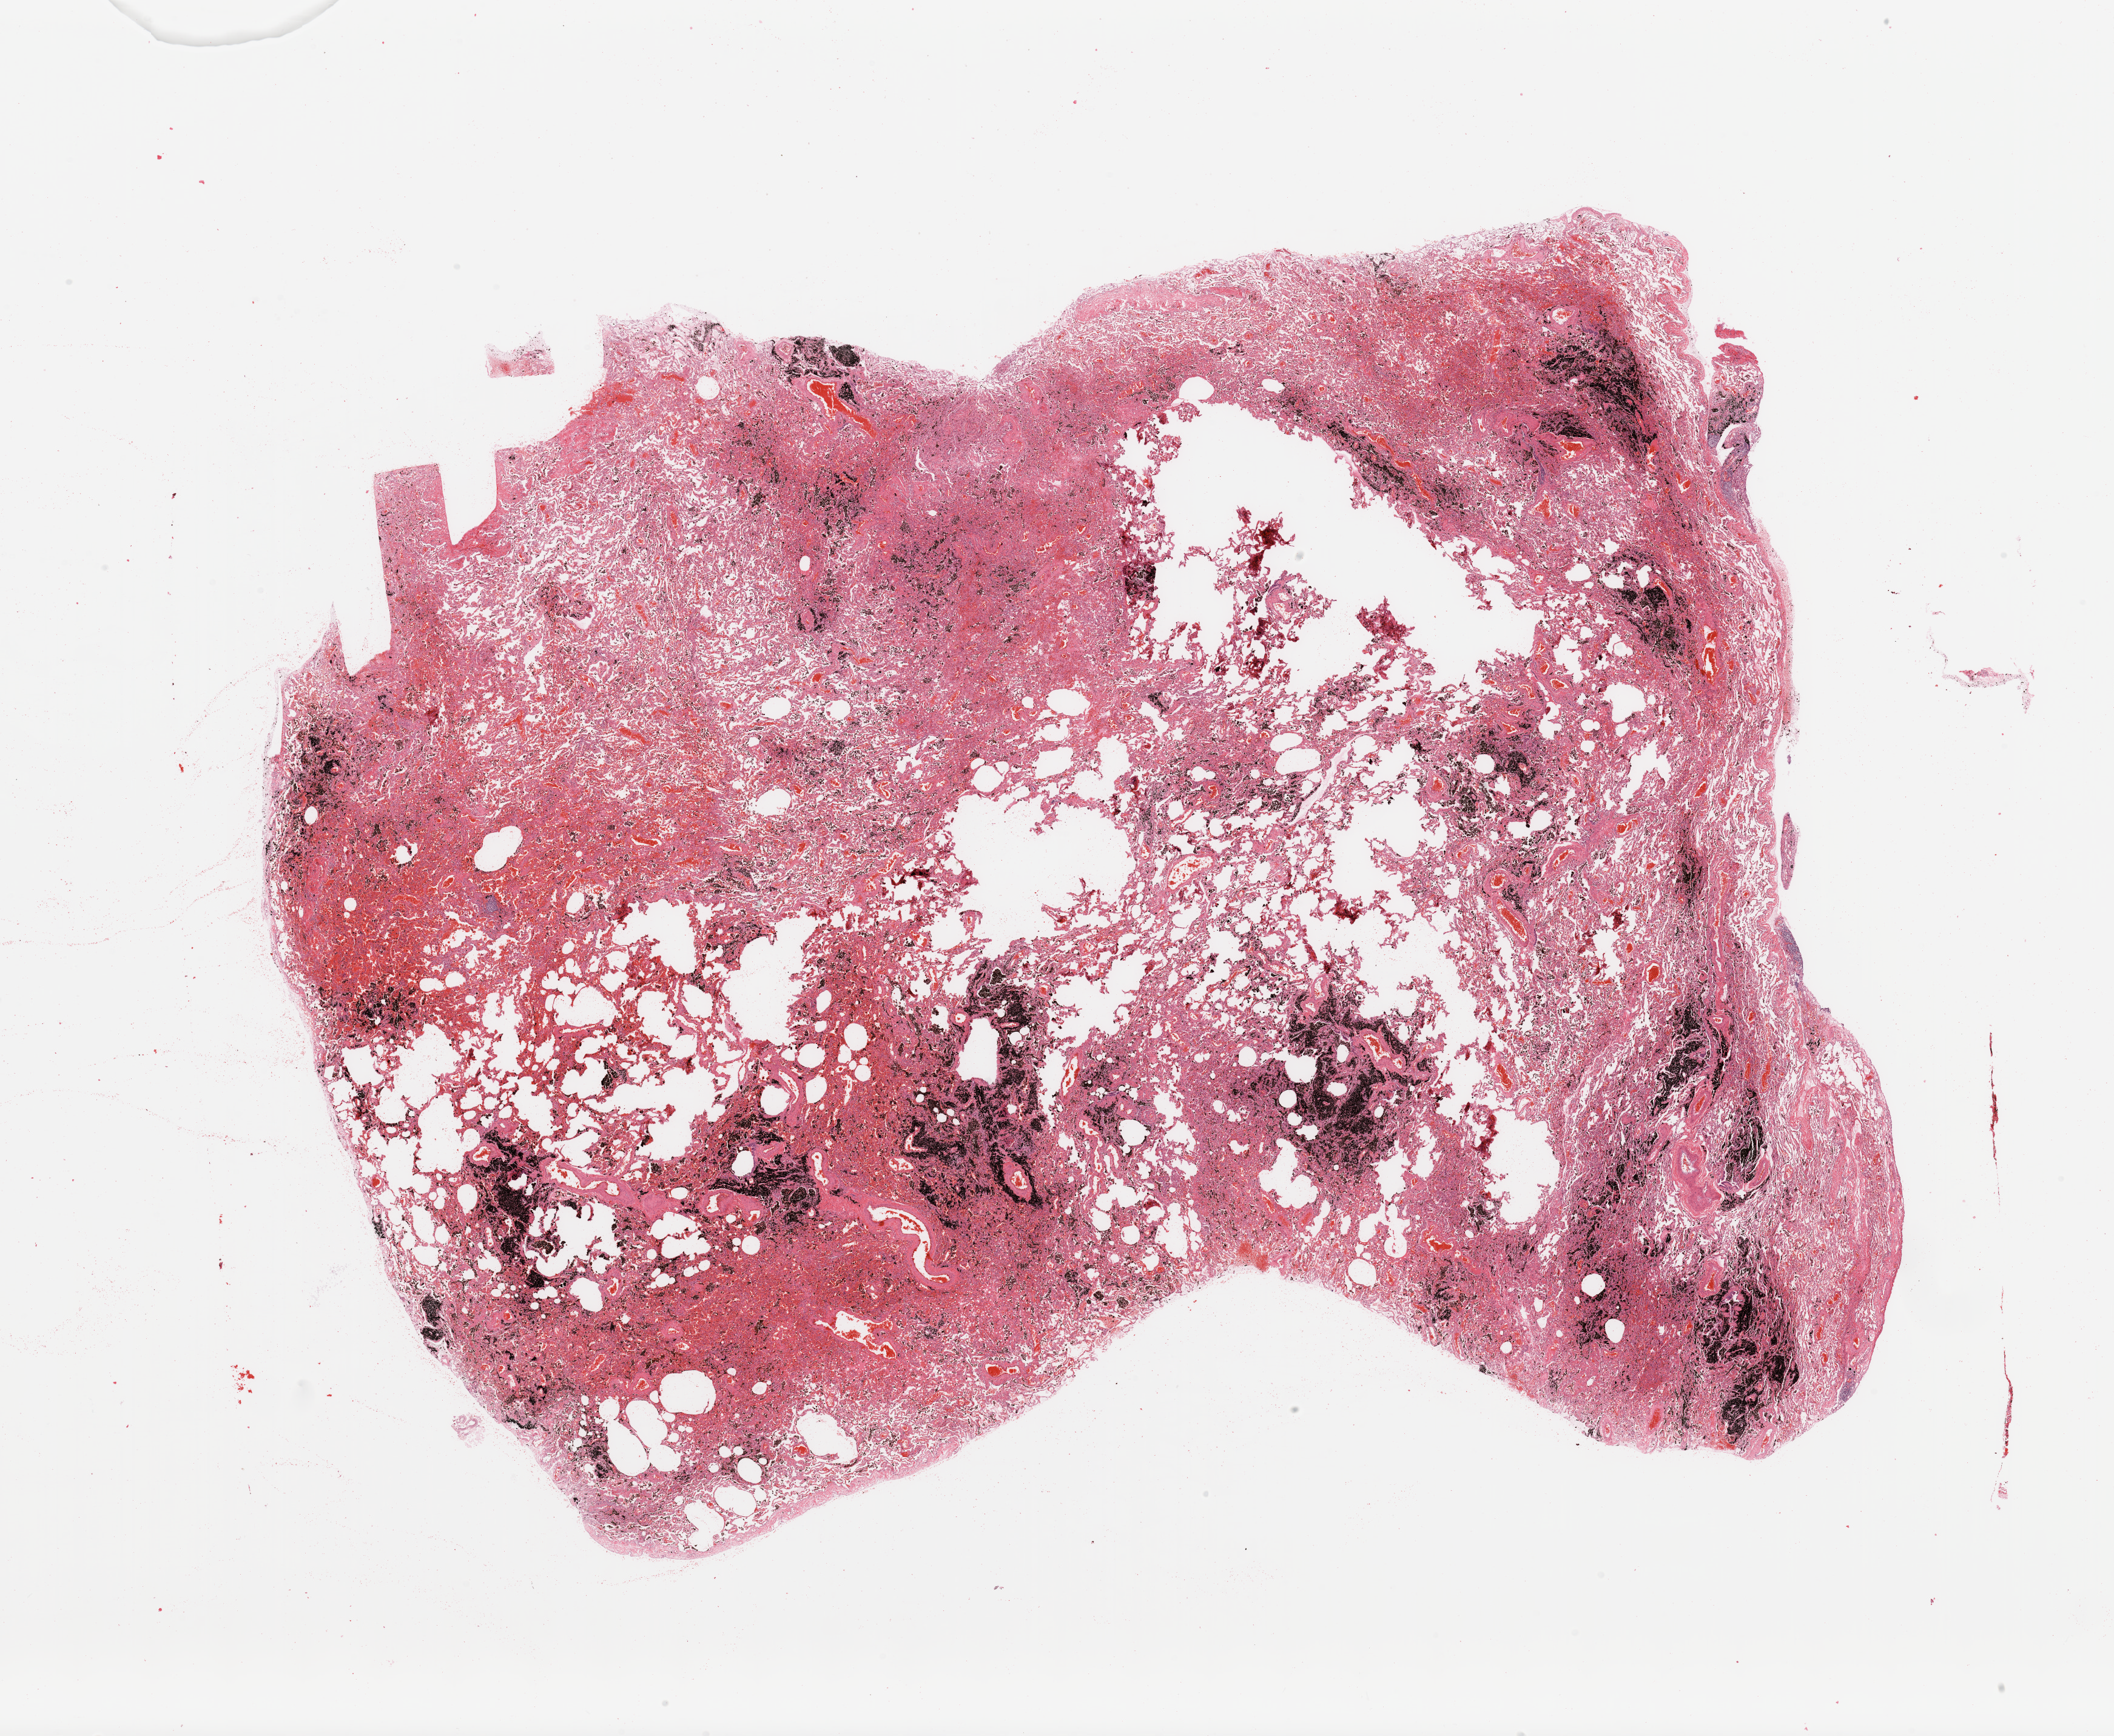
Digitized H&E-stained tissue section (whole slide), whole scanned area (about 27.6 x 22.6 mm, from a 20x scan) shown as a low-resolution overview. Lung, normal (non-tumour) tissue. Male, 56 y/o.
- this section: normal (non-tumour) tissue from the same patient
- patient diagnosis: Adenocarcinoma, NOS